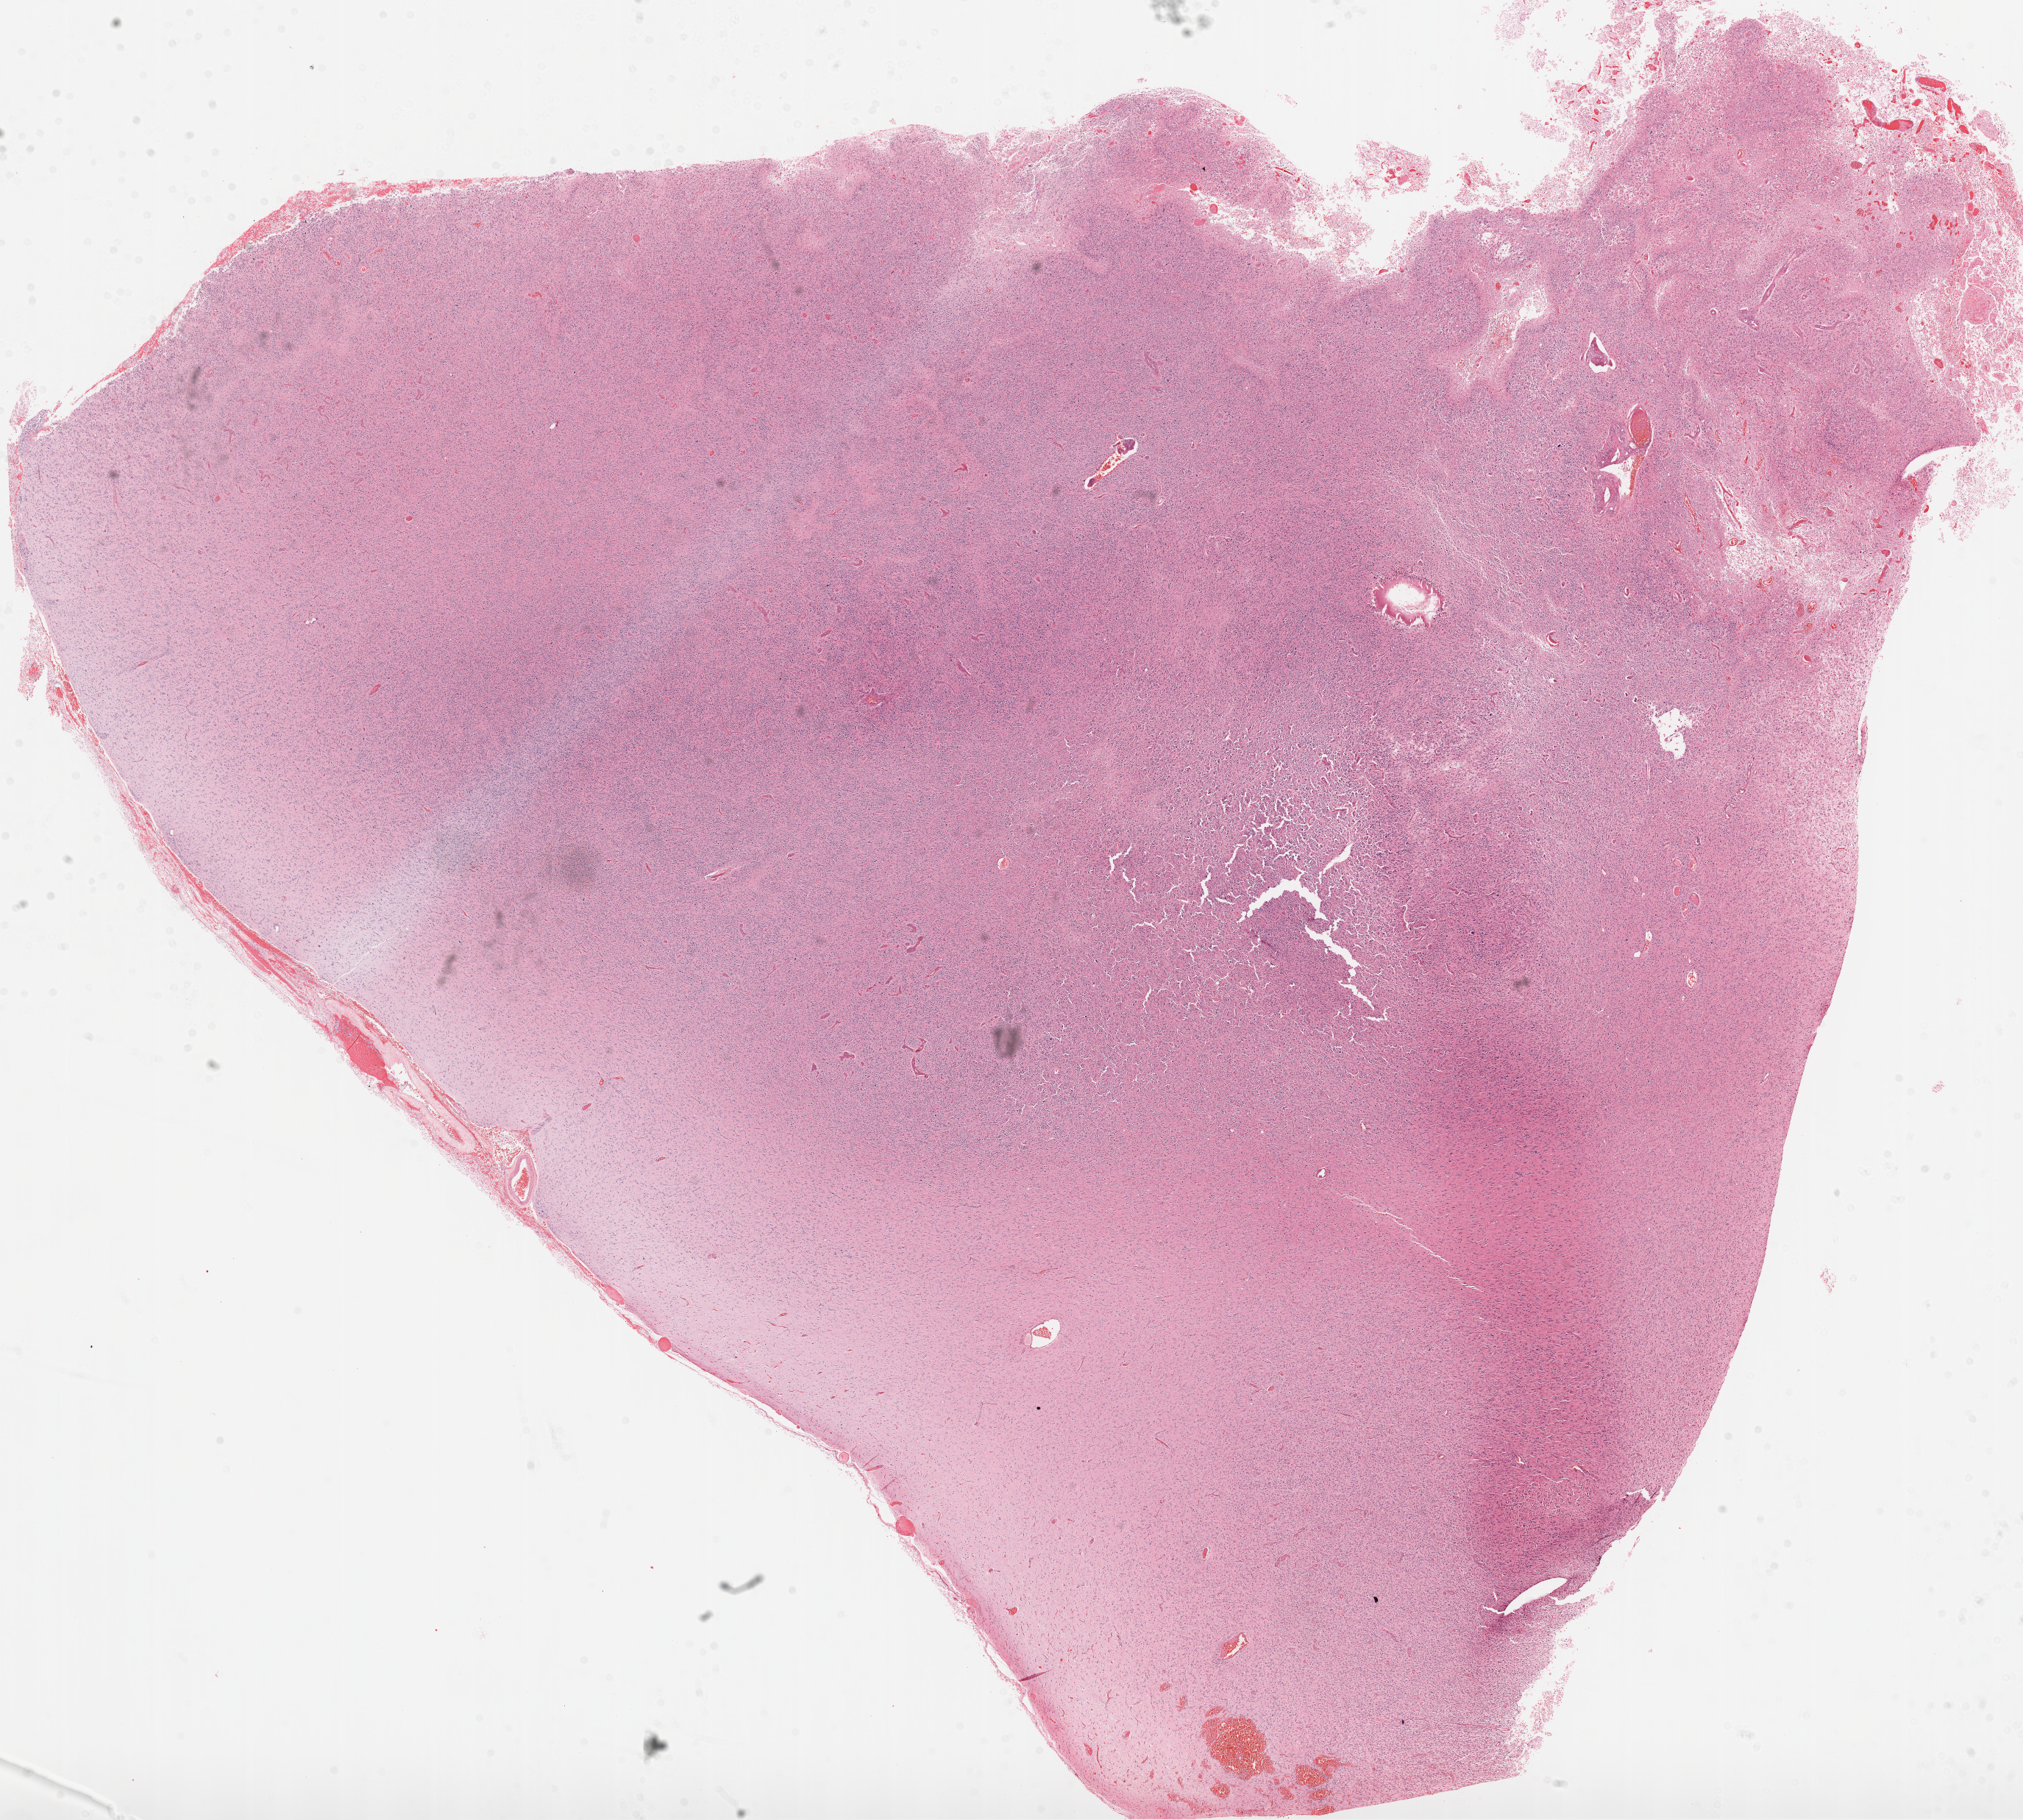
Whole-slide histology image, H&E, a low-resolution overview of the entire scanned area, about 22.1 x 19.9 mm (from a 20x scan), formalin-fixed paraffin-embedded (FFPE) diagnostic section, brain, primary tumour sample. Male patient; age at initial diagnosis 60 years.
Diagnosis: Glioblastoma.